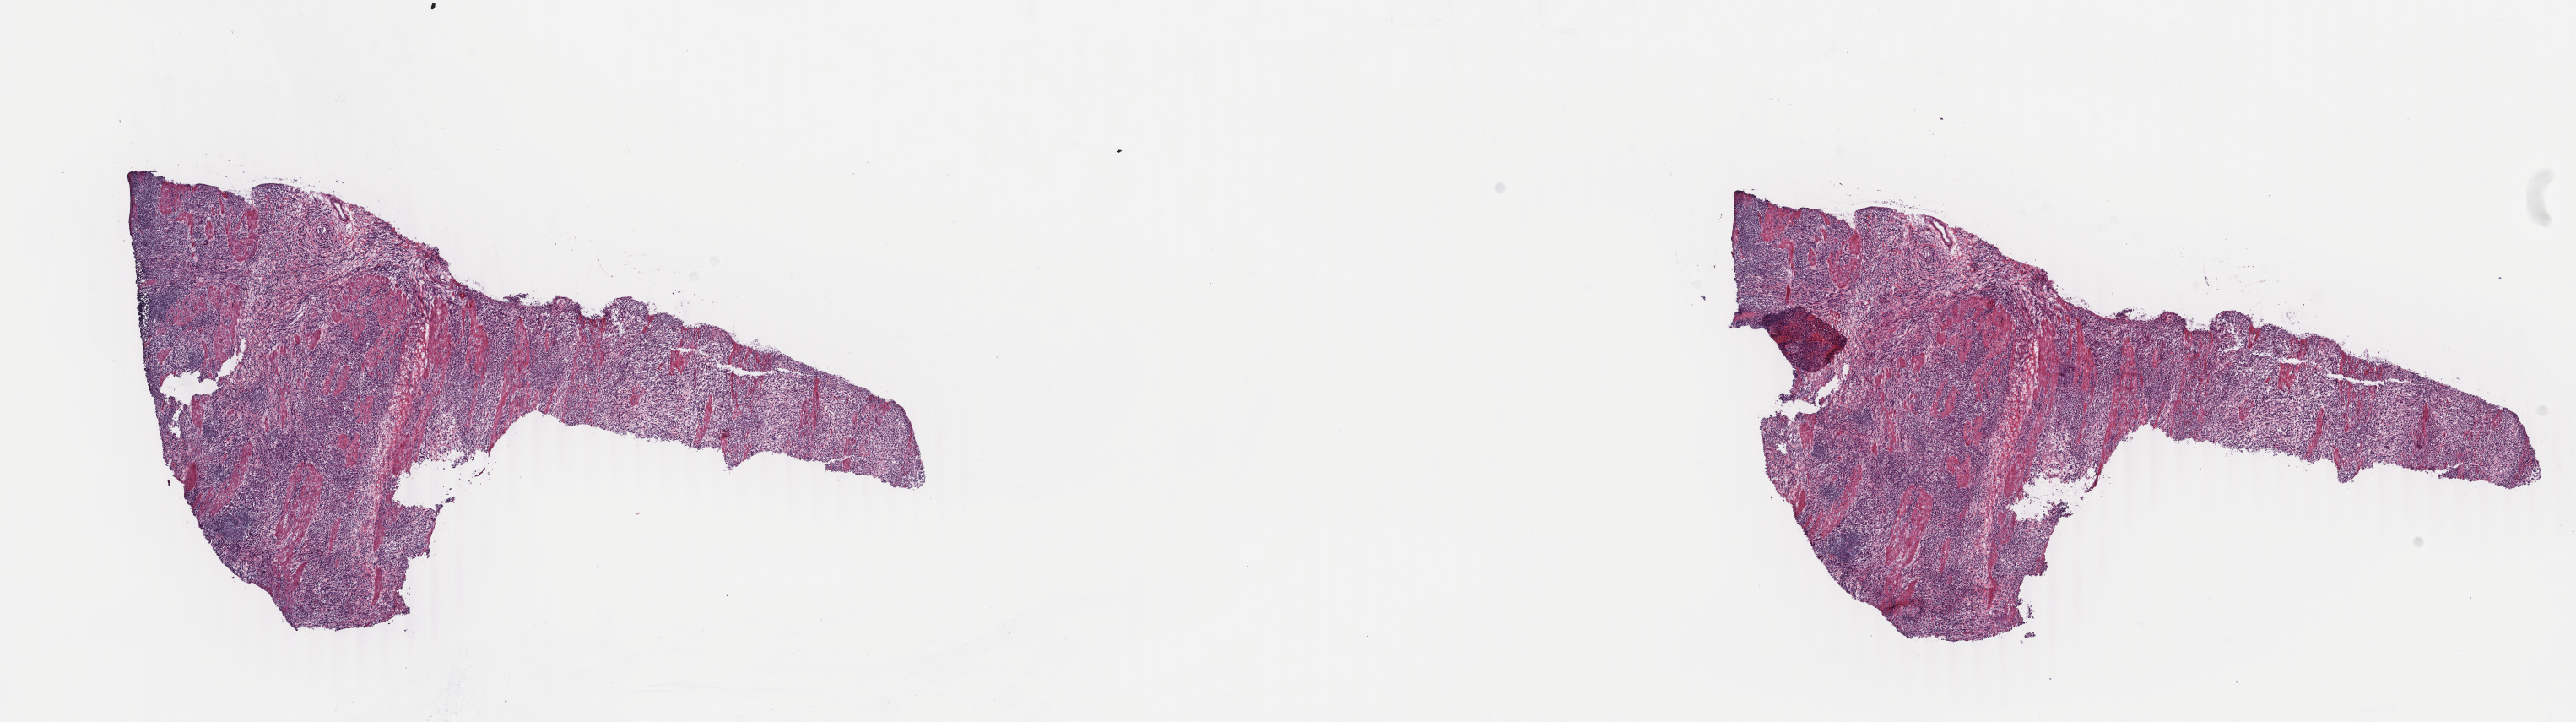
Hematoxylin and eosin (H&E) stained whole-slide image, shown as a low-resolution overview of the whole scanned area (about 24.3 x 6.8 mm, slide scanned at 40x). Frozen section from the top of the tissue portion. Sample: primary tumour, stomach. Patient: female, age at initial diagnosis 69 years. Histologic grade: G3 (poorly differentiated). Slide review estimates, as recorded: tumour cells 65%, tumour nuclei 70%, normal cells 0%, stromal cells 33%, necrosis 2%. Infiltration values recorded for this section: lymphocyte infiltration 15%, monocyte infiltration 2%, neutrophil infiltration 4%.
Lymph nodes positive (case pathology): 2 of 8 examined. Pathologic diagnosis: Tubular adenocarcinoma (gastric antrum). AJCC pathologic stage: IIB.